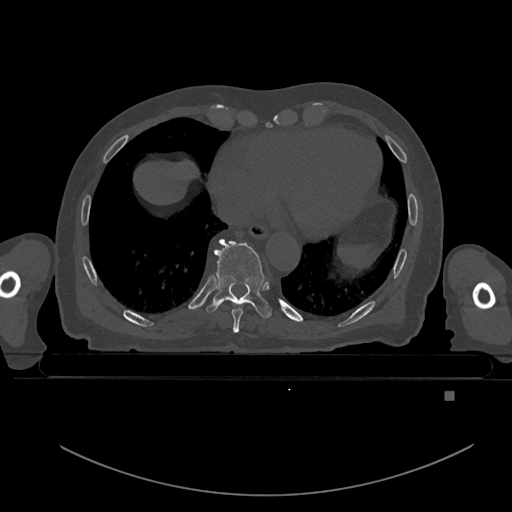
CT including the spine, one axial slice. Position 162 of 969 along the scan axis. Bone window (W 1800 / L 400 HU). 0.5 mm slice thickness. 512 × 512 image matrix, field of view 456 × 456 mm. Male patient, age 82 years. Case-level facts recorded for this patient, not image findings: primary cancer: prostate; vertebrae with lytic lesions (as recorded): T11, T9, T8, T2.
Outlined on this slice (semi-automatically segmented with operator editing):
- T8 vertebra: bounding box <232,299,246,333> (left, top, right, bottom; pixels)
- T9 vertebra: <206,239,272,318>